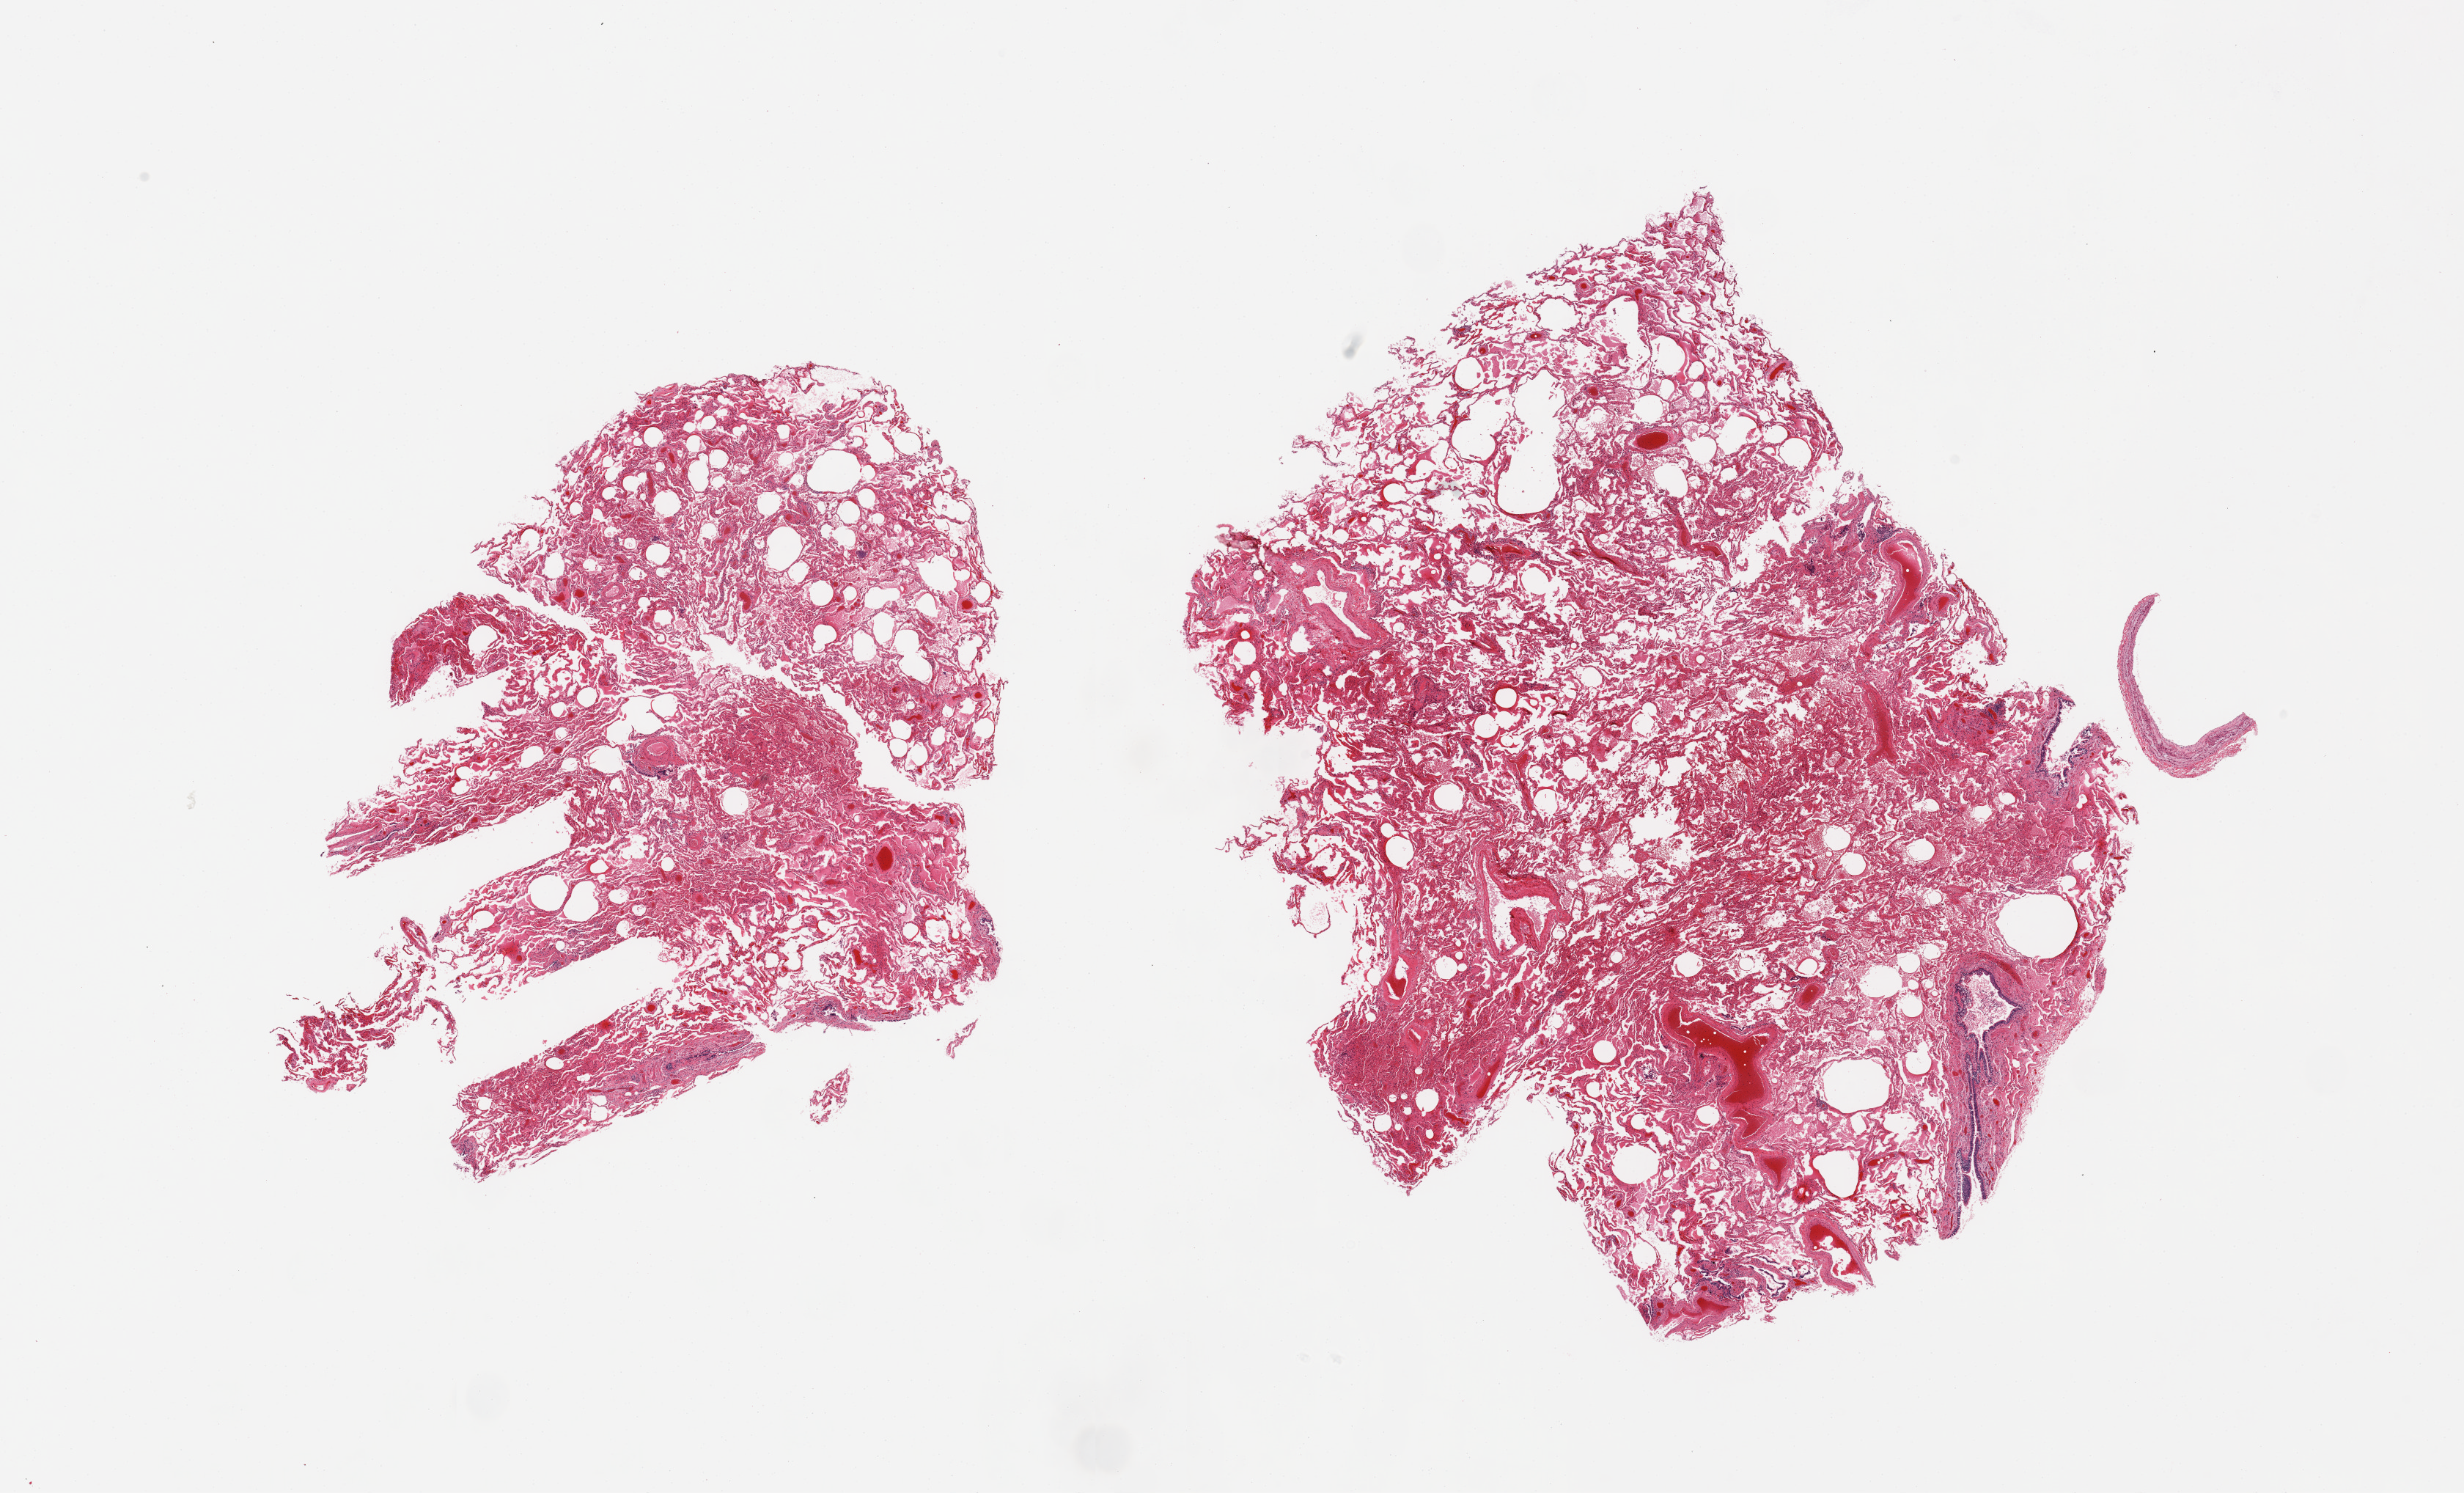
Digitized haematoxylin and eosin-stained section, brightfield, low-resolution overview of the scanned area, about 26.6 x 16.1 mm (acquisition: 20x scan), PAXgene-fixed, paraffin-embedded tissue, section of lung (target tissue), donor tissue sample.
Pathologist's review note for this sample: 2 pieces; congestion, hemorrhage, and edema; one piece is oversized.